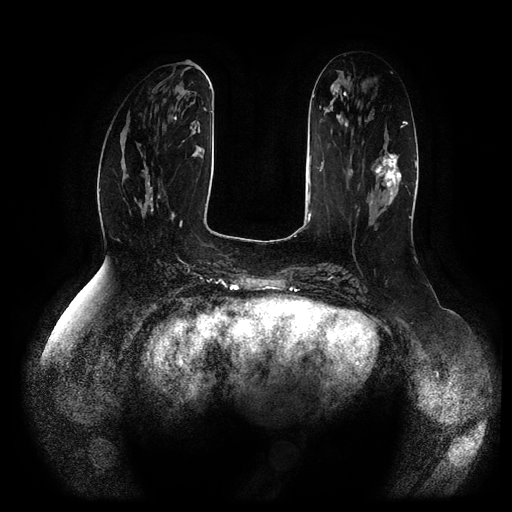
Breast MRI (dynamic contrast-enhanced, multi-phase), one axial slice; position 35 of 116 along the scan axis; dynamic contrast-enhanced series, time point 2 of 5 at this slice position (early post-contrast); 1.5 T; TE 2.5 ms, TR 5.2 ms; 2 mm slice thickness; 512 × 512 image matrix, field of view 400 × 400 mm. Female patient, age 66 years.
Outlined on this slice (semi-automatic segmentation, software-assisted and operator-edited):
- breast lesion (labelled 'tumour' in the annotation; benign lesions carry a separate 'benign' label): bounding box <375,153,401,210> (left, top, right, bottom; pixels)